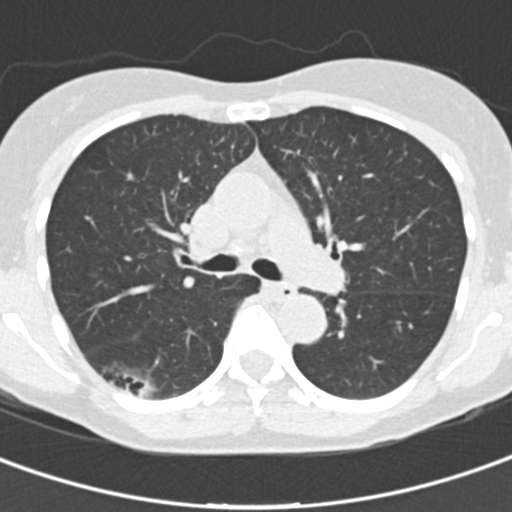
Low-dose screening chest CT, one axial slice. Slice 98 of 162 in the series (ordered by position). Reconstruction kernel B30f. 120 kVp. Lung window (W 1500 / L -600 HU). 2 mm slice thickness. 512 × 512 image matrix, field of view 276 × 276 mm.
Outlined on this slice (outlined manually by an expert reader):
- lesion 1 (tumor, lower lobe of right lung): bounding box (x1, y1, x2, y2) in pixels: (139, 384, 152, 398)